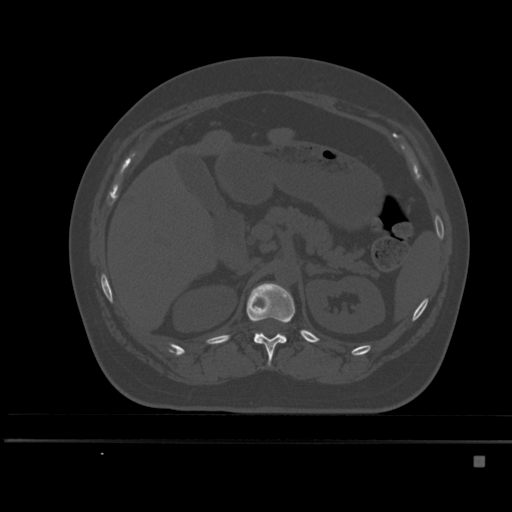
CT including the spine, one axial slice. Position 210 of 495 along the scan axis. Bone window (W 1800 / L 400 HU). 1.5 mm slice thickness. 512 × 512 image matrix. Female patient, age 33 years. From the clinical record (not read from this slice): primary cancer: breast.
Outlined on this slice (semi-automatically segmented with operator editing):
- T12 vertebra: bounding box [x1, y1, x2, y2] px = [246, 283, 295, 366]